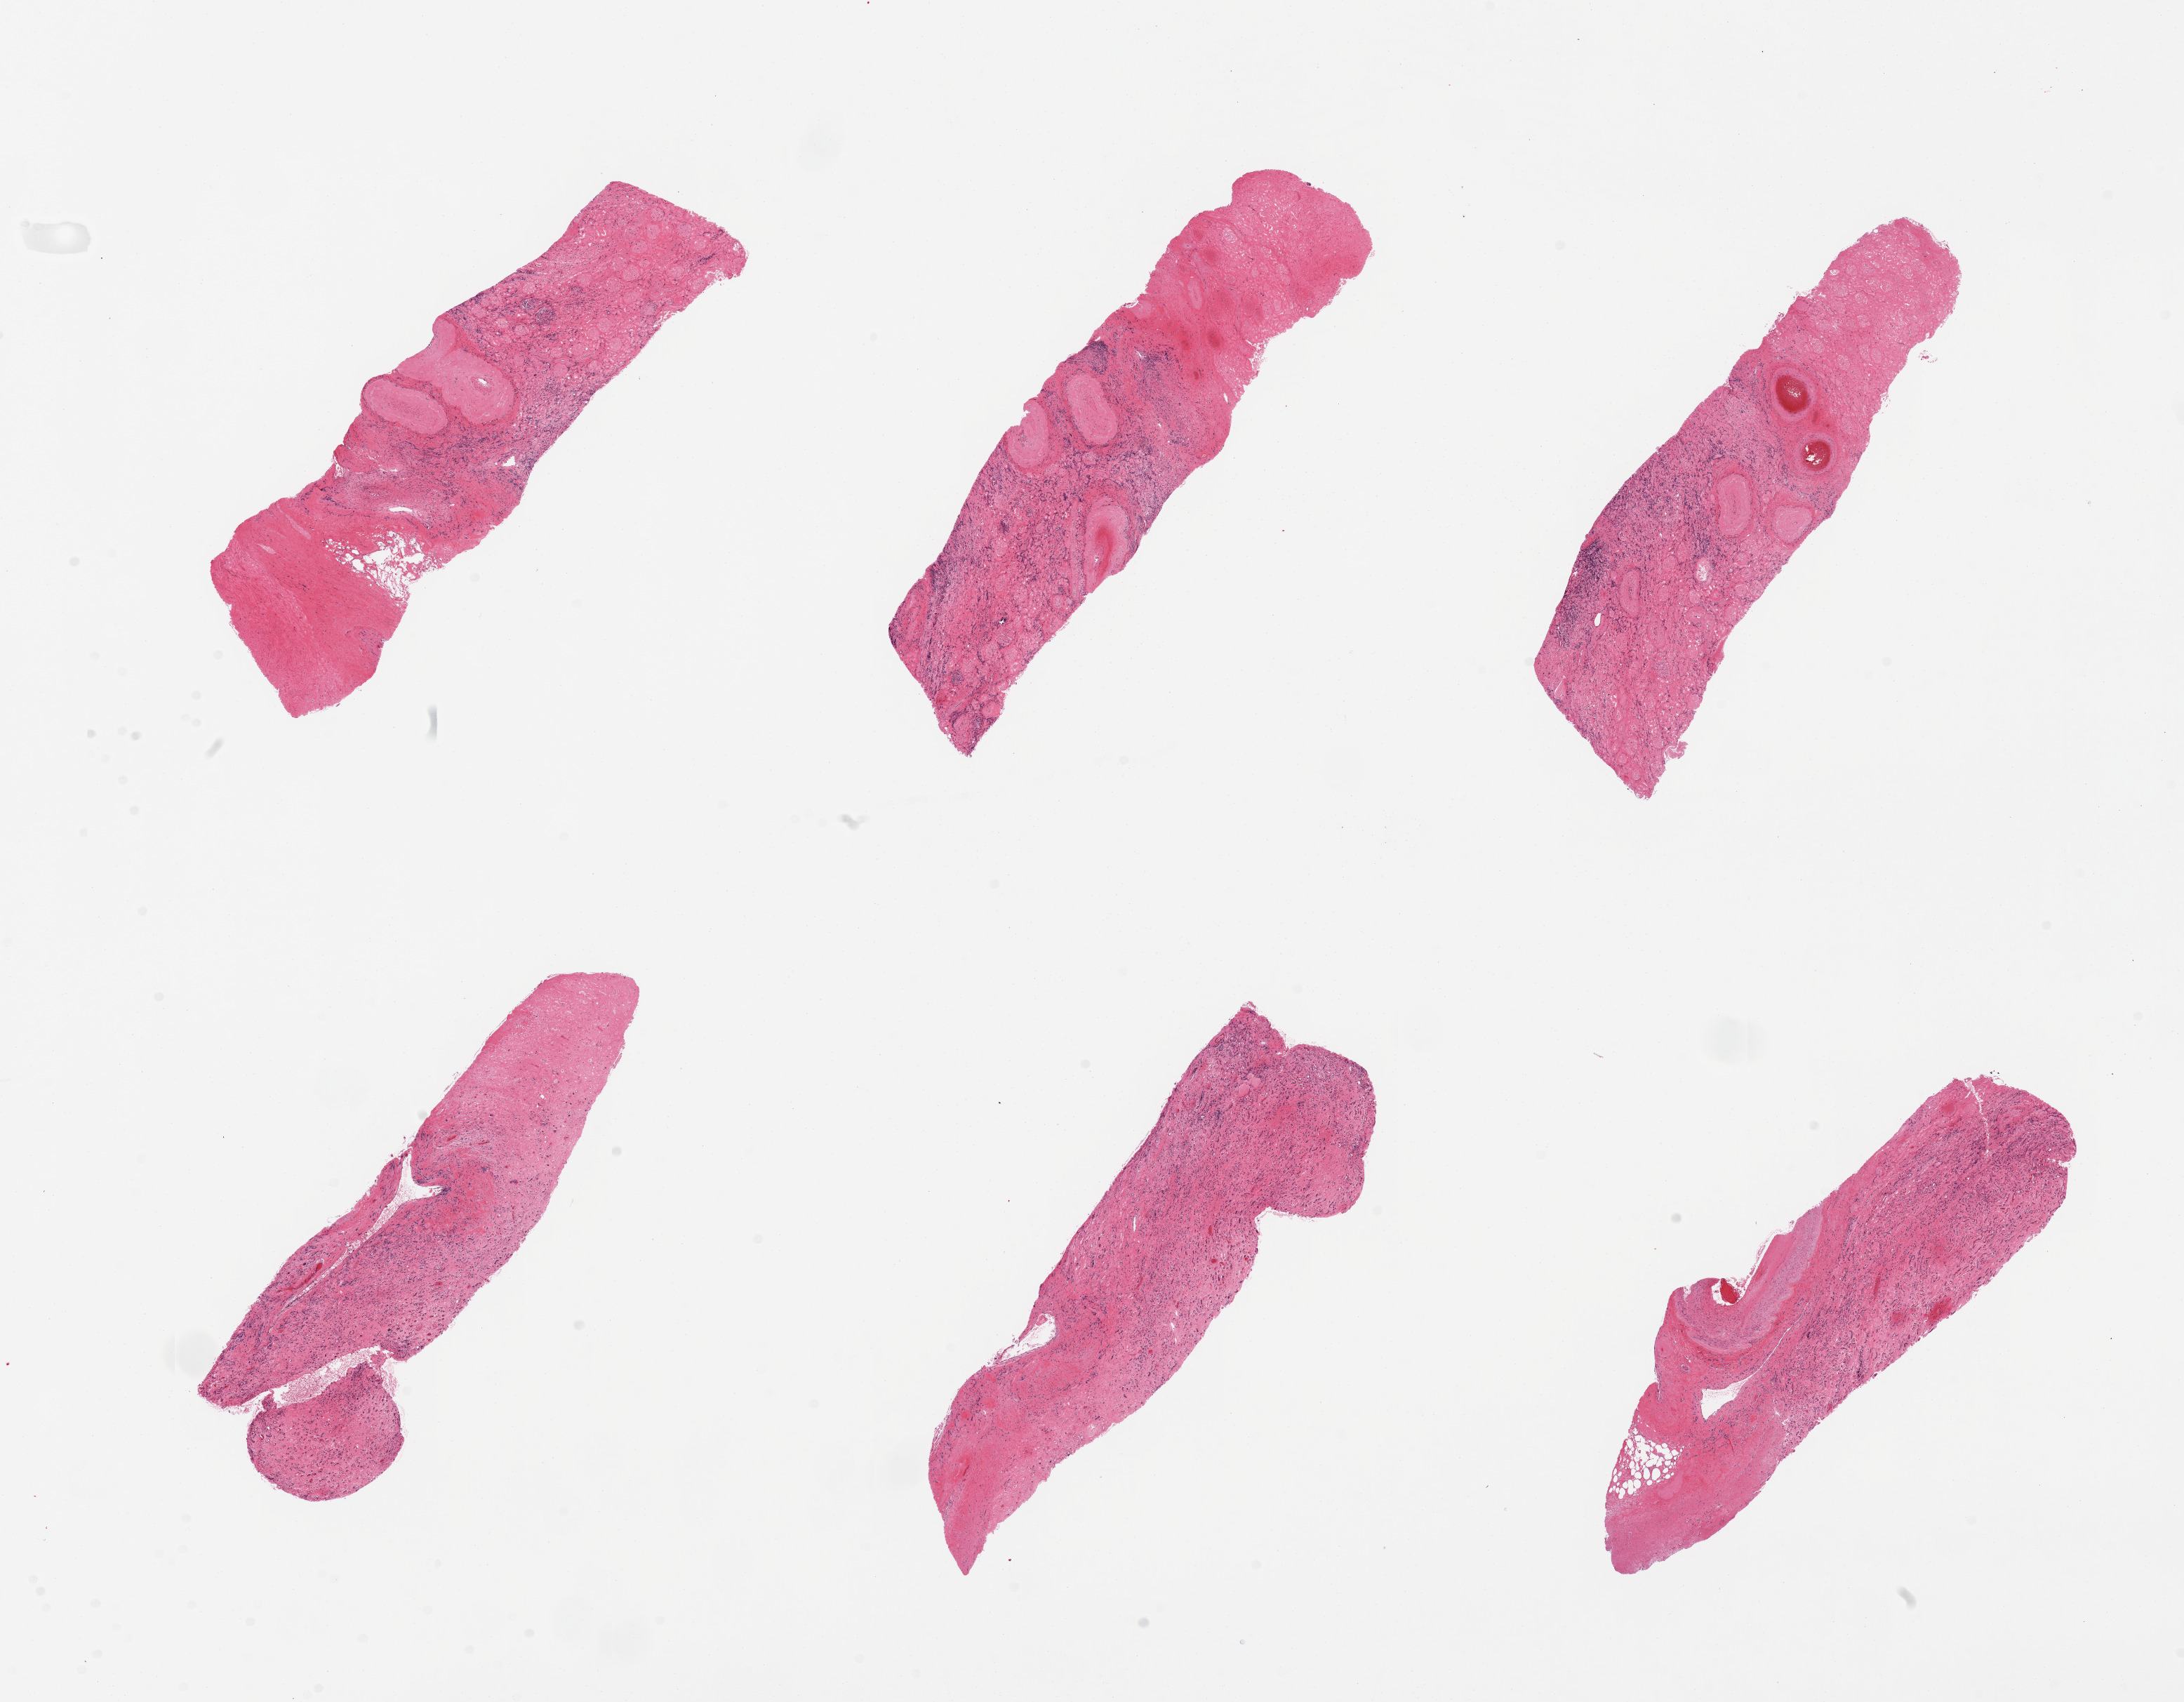
Digitized haematoxylin and eosin-stained section, brightfield — shown as a low-resolution overview of the whole scanned area (about 24.6 x 19.2 mm). Male donor.
Specimen: PAXgene-fixed paraffin-embedded (PFPE) section; target tissue: renal cortex; donor tissue sample.